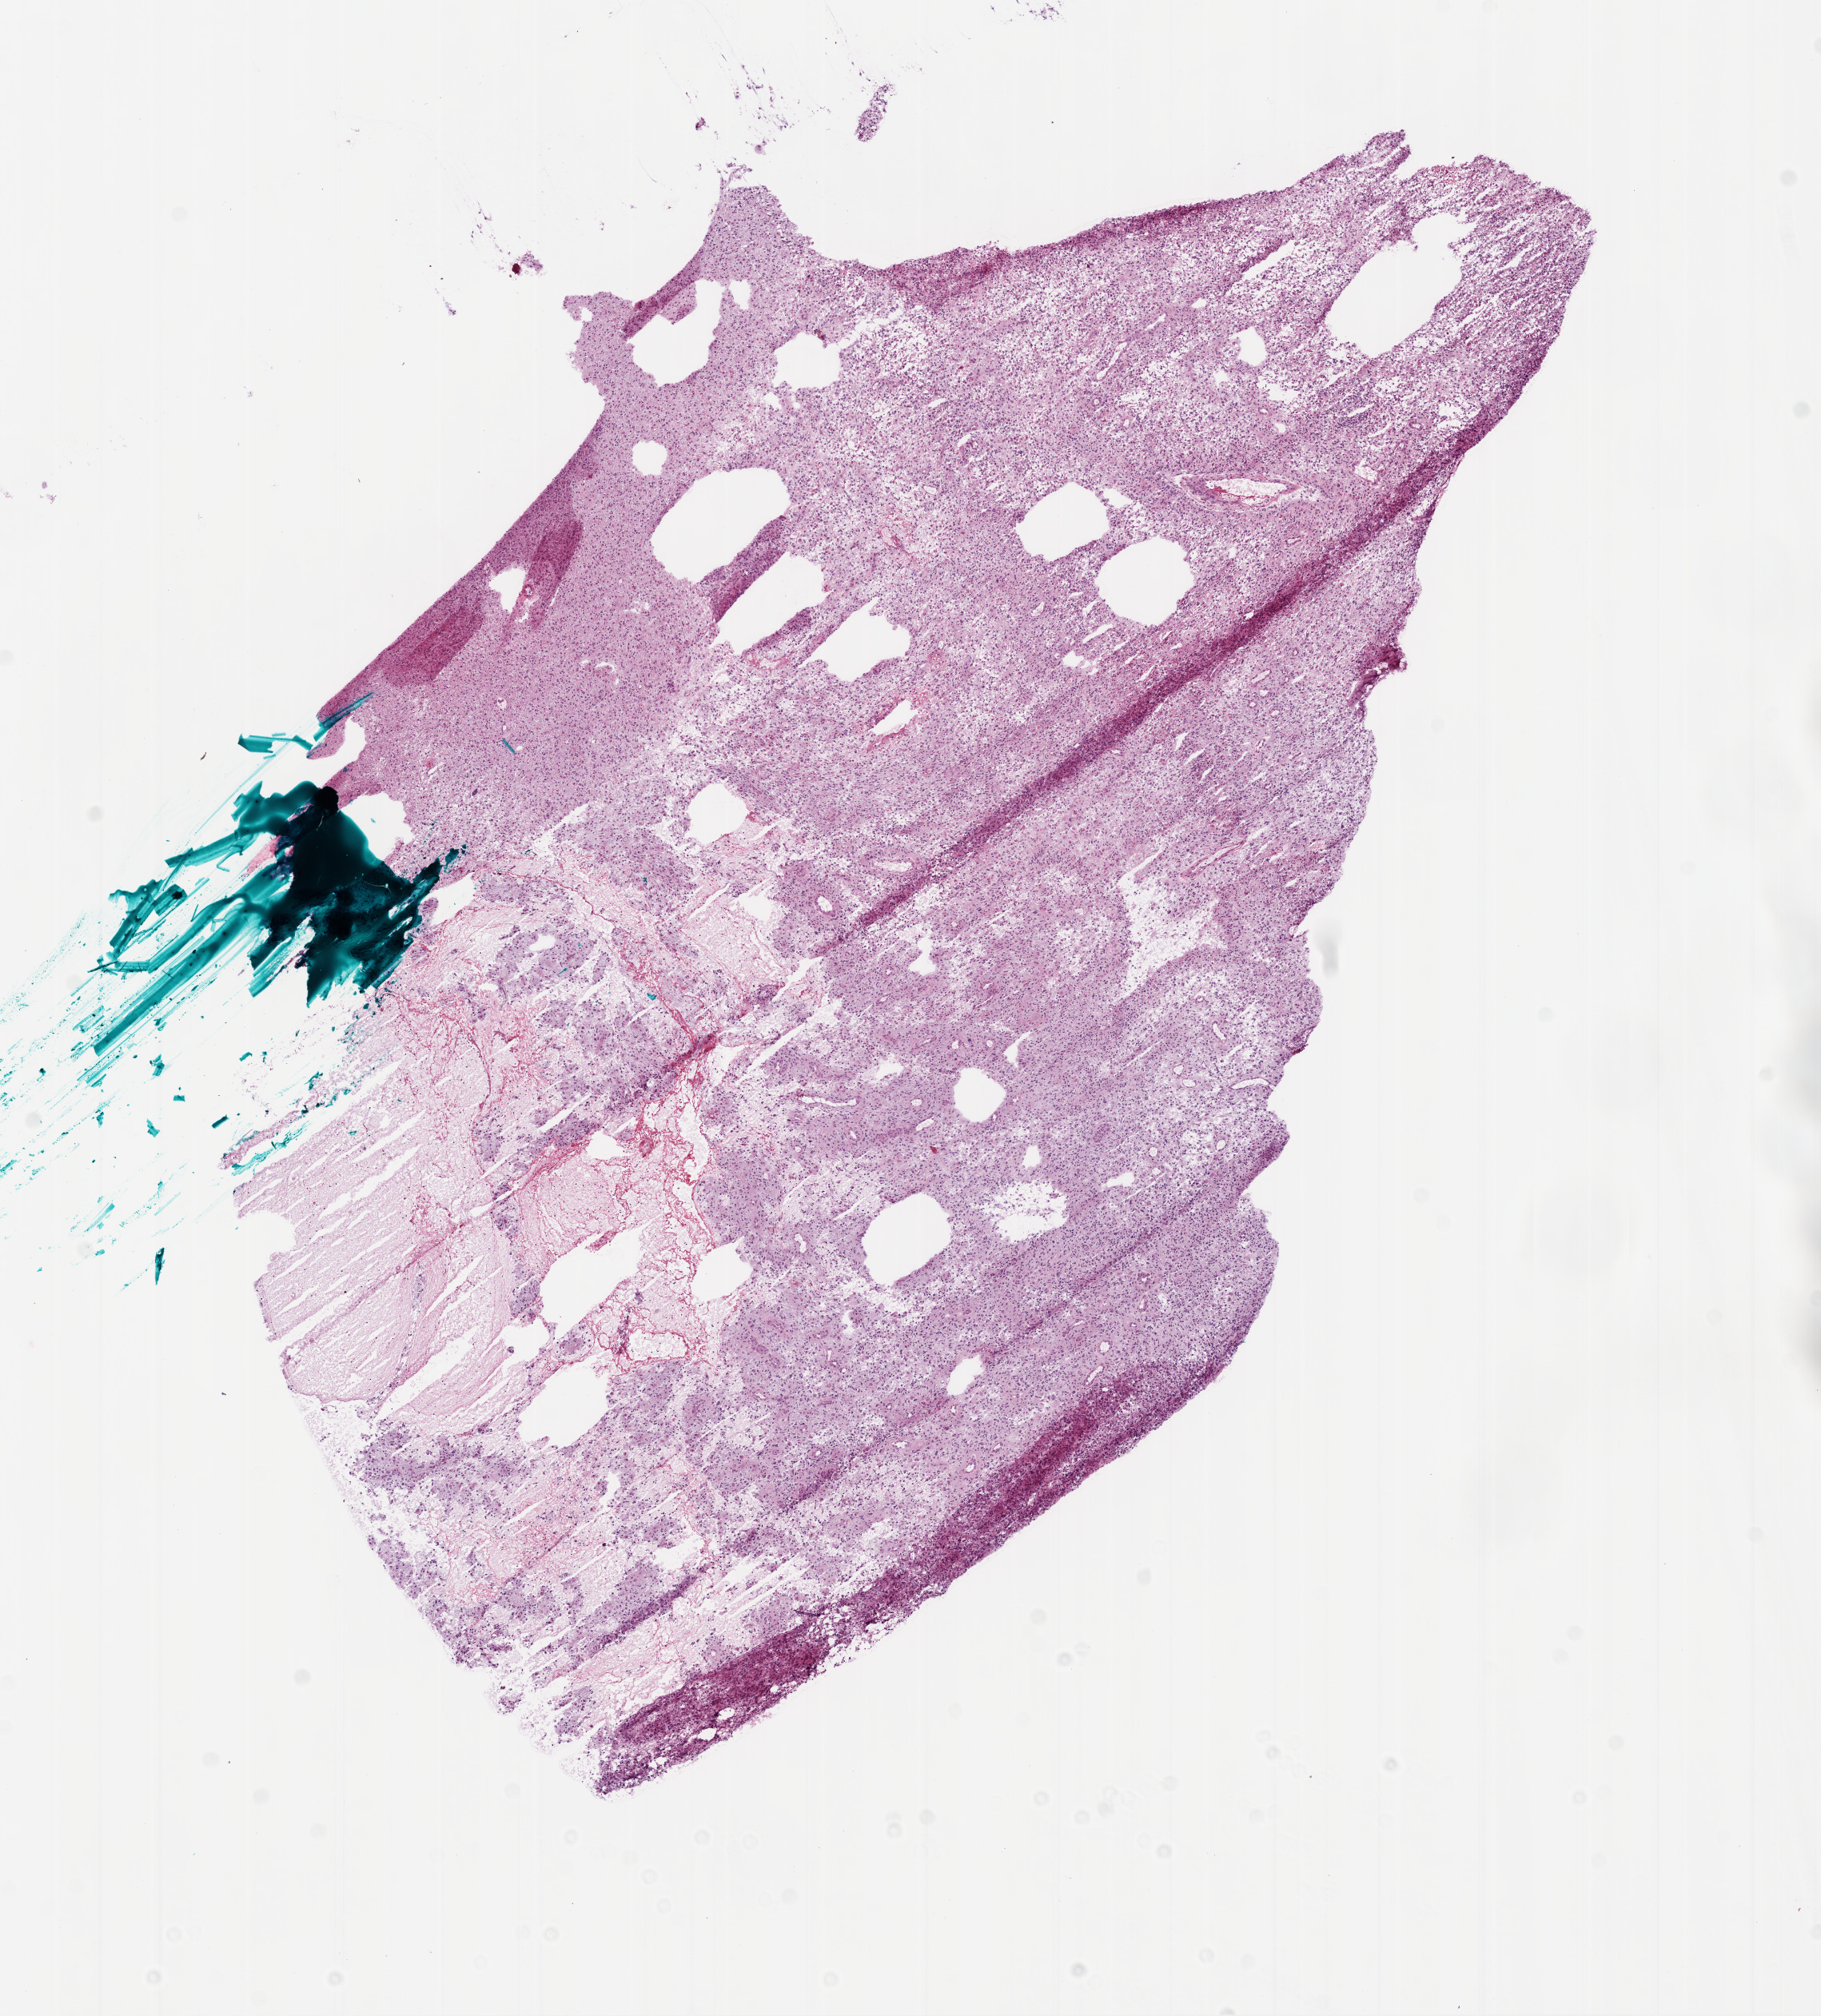
H&E whole-slide image, a low-resolution overview of the entire scanned area, about 9.2 x 10.2 mm; frozen section; primary tumour sample from the brain. Patient: male, age at initial diagnosis 60 years. Slide review estimates, as recorded: tumour cells 95%, tumour nuclei 100%, normal cells 0%, stromal cells 0%, necrosis 5%.
Histologic diagnosis: Glioblastoma.